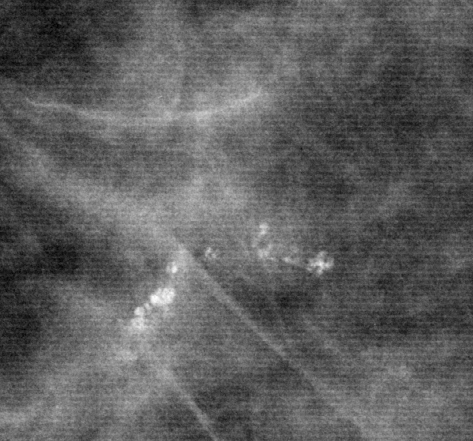
Crop from a digitized film mammogram around one marked abnormality, right breast, CC view, BI-RADS breast density category 2 (scale 1–4).
Calcifications, morphology pleomorphic, distribution clustered; BI-RADS assessment category 4; pathology result (as recorded, not read from the image): benign.